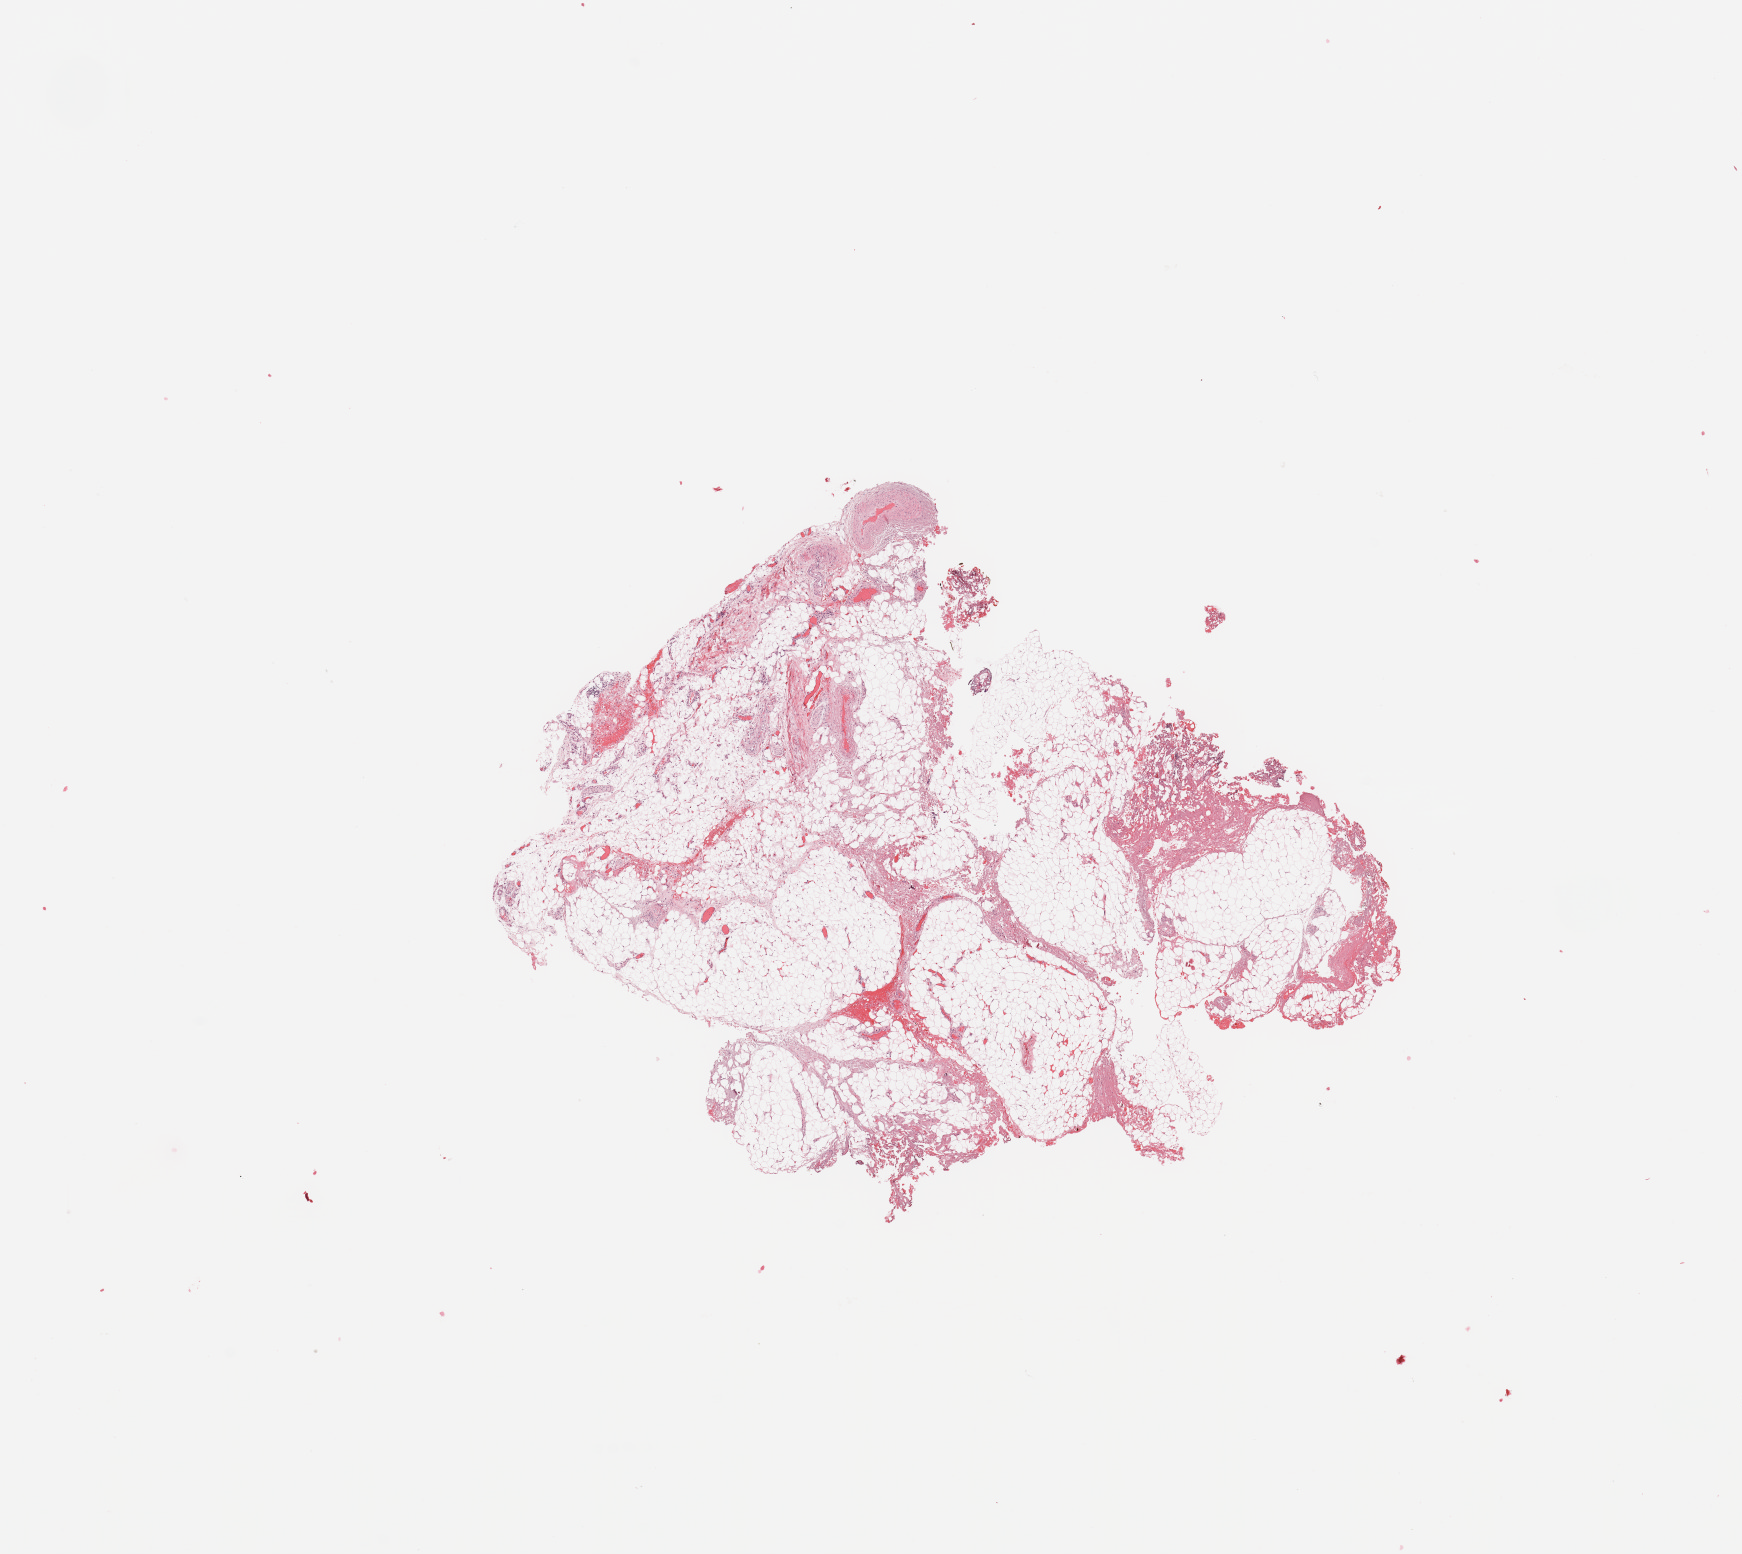
Digitized H&E tissue section (whole slide) — whole scanned area (about 13.8 x 12.3 mm, acquisition: 20x scan) shown as a low-resolution overview, normal (non-tumour) tissue sample. Patient: female, age 67 years.
This section: normal (non-tumour) tissue from the same patient. Patient diagnosis (cohort enrolment): sarcoma (site not recorded at cohort level).